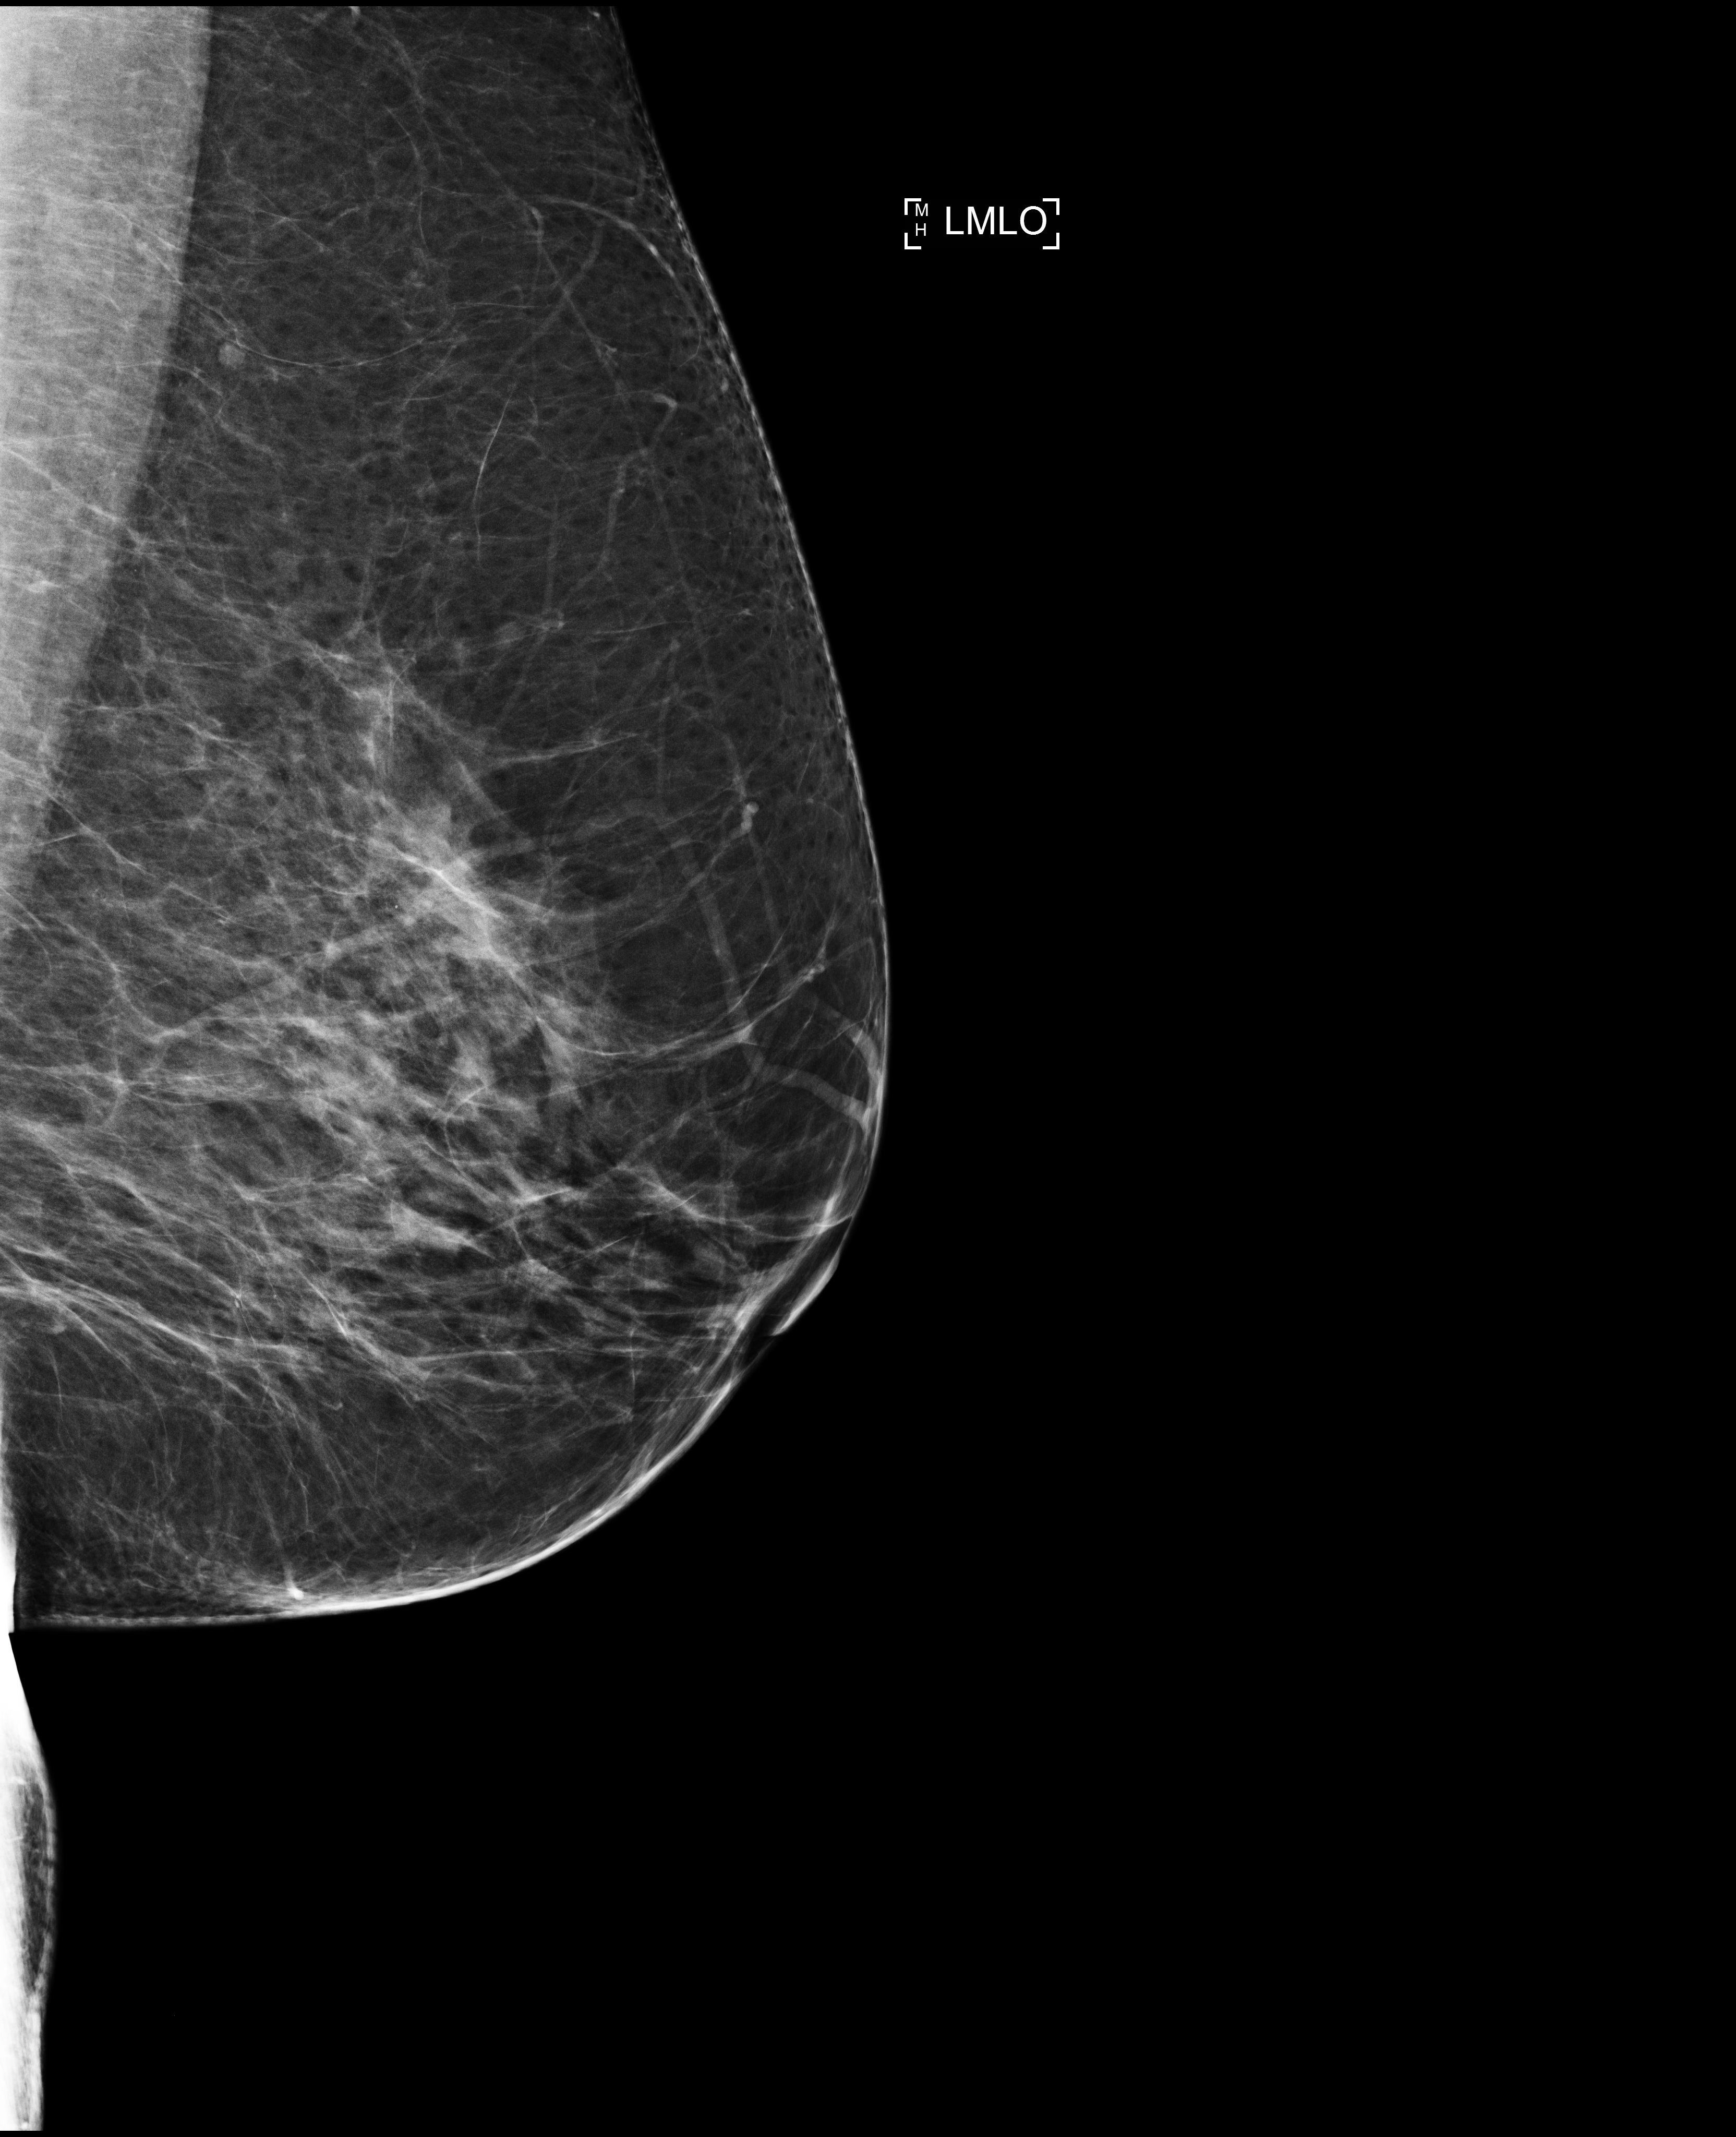
Screening examination. Patient aged 57 years (female).
Image type: full-field digital mammogram. Breast: left. Projection: MLO view.